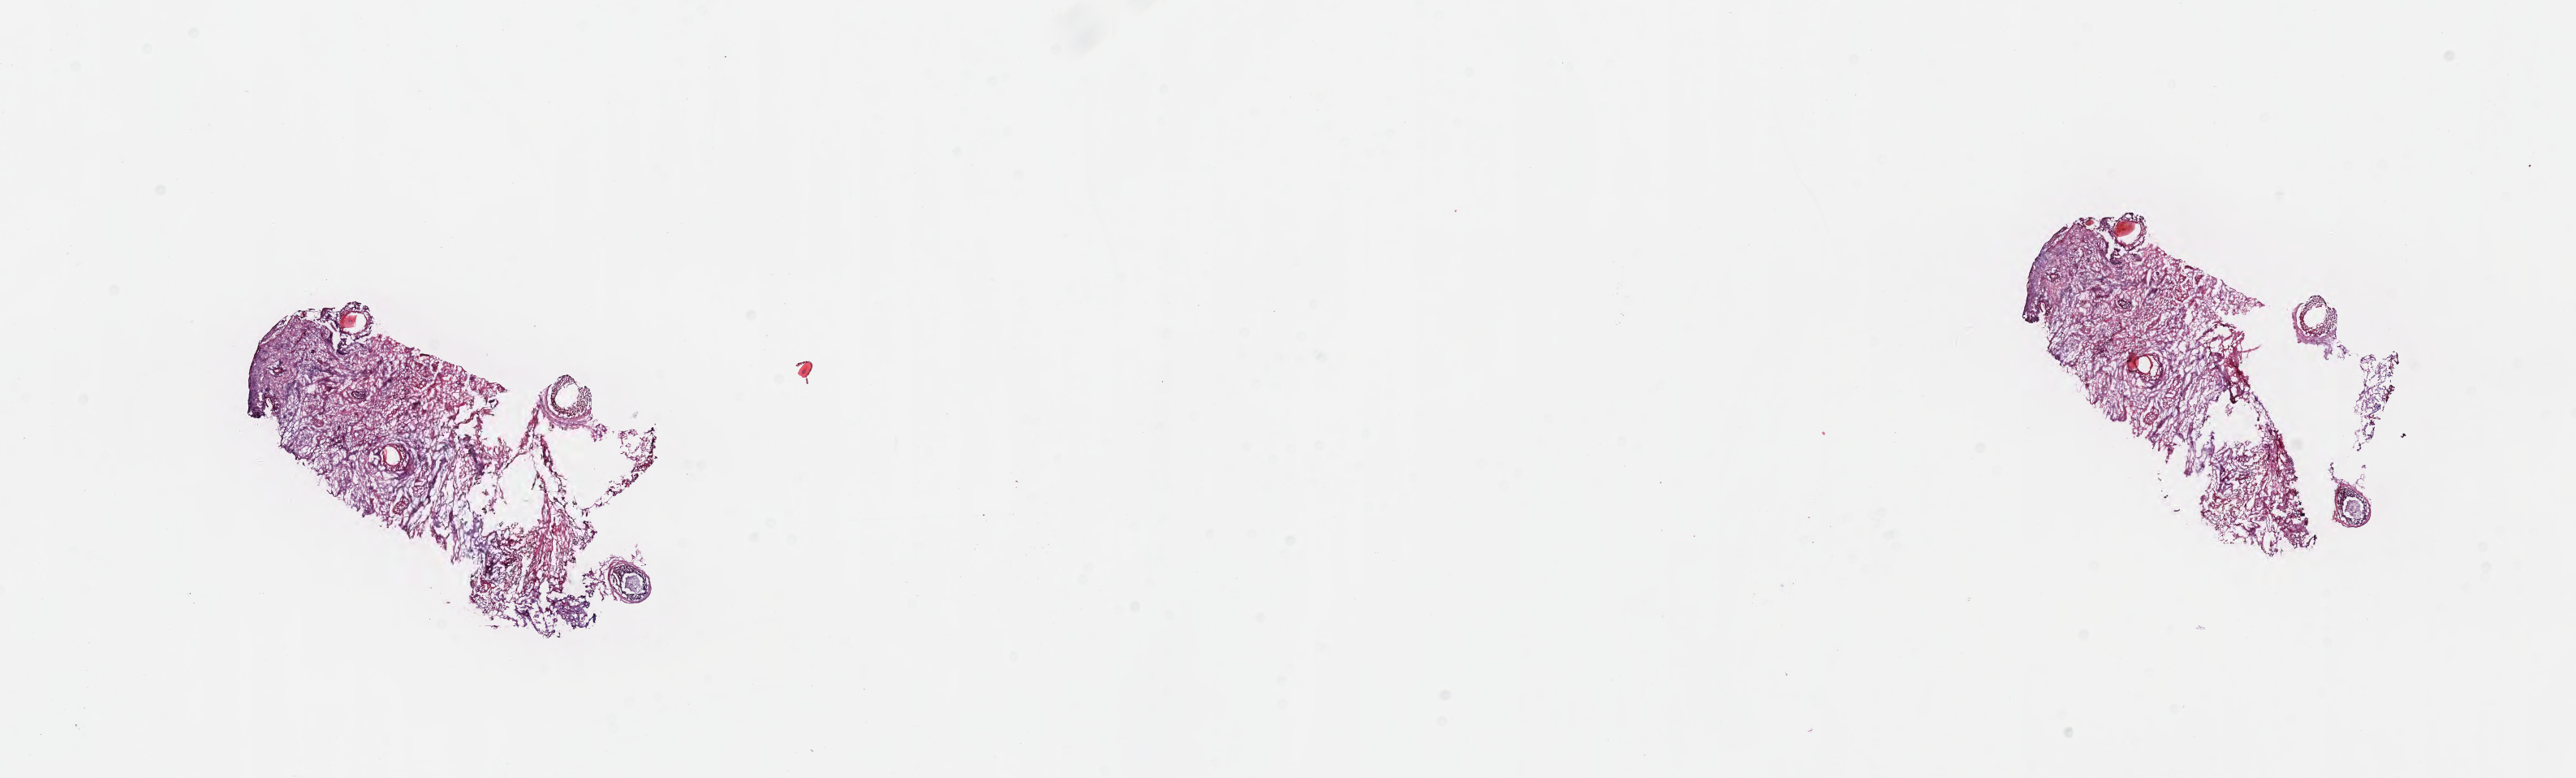
Digitized hematoxylin and eosin (H&E)-stained section, shown as a low-resolution overview of the whole scanned area (about 25.7 x 7.7 mm). Frozen section (tissue freezing medium). Non-tumor (normal tissue) sample from a patient with squamous cell carcinoma, NOS. Site: lower gum (left). Male patient. Slide review estimates, as recorded: tumor cells 0%, tumor nuclei 0%, stromal cells 0%, necrosis 0%, normal cells 100%. Infiltration values recorded for this section: lymphocyte infiltration 0%, monocyte infiltration 0%, neutrophil infiltration 0%.
This section: non-tumor tissue sample; the patient's diagnosis is given above. Section: top of the tissue portion.